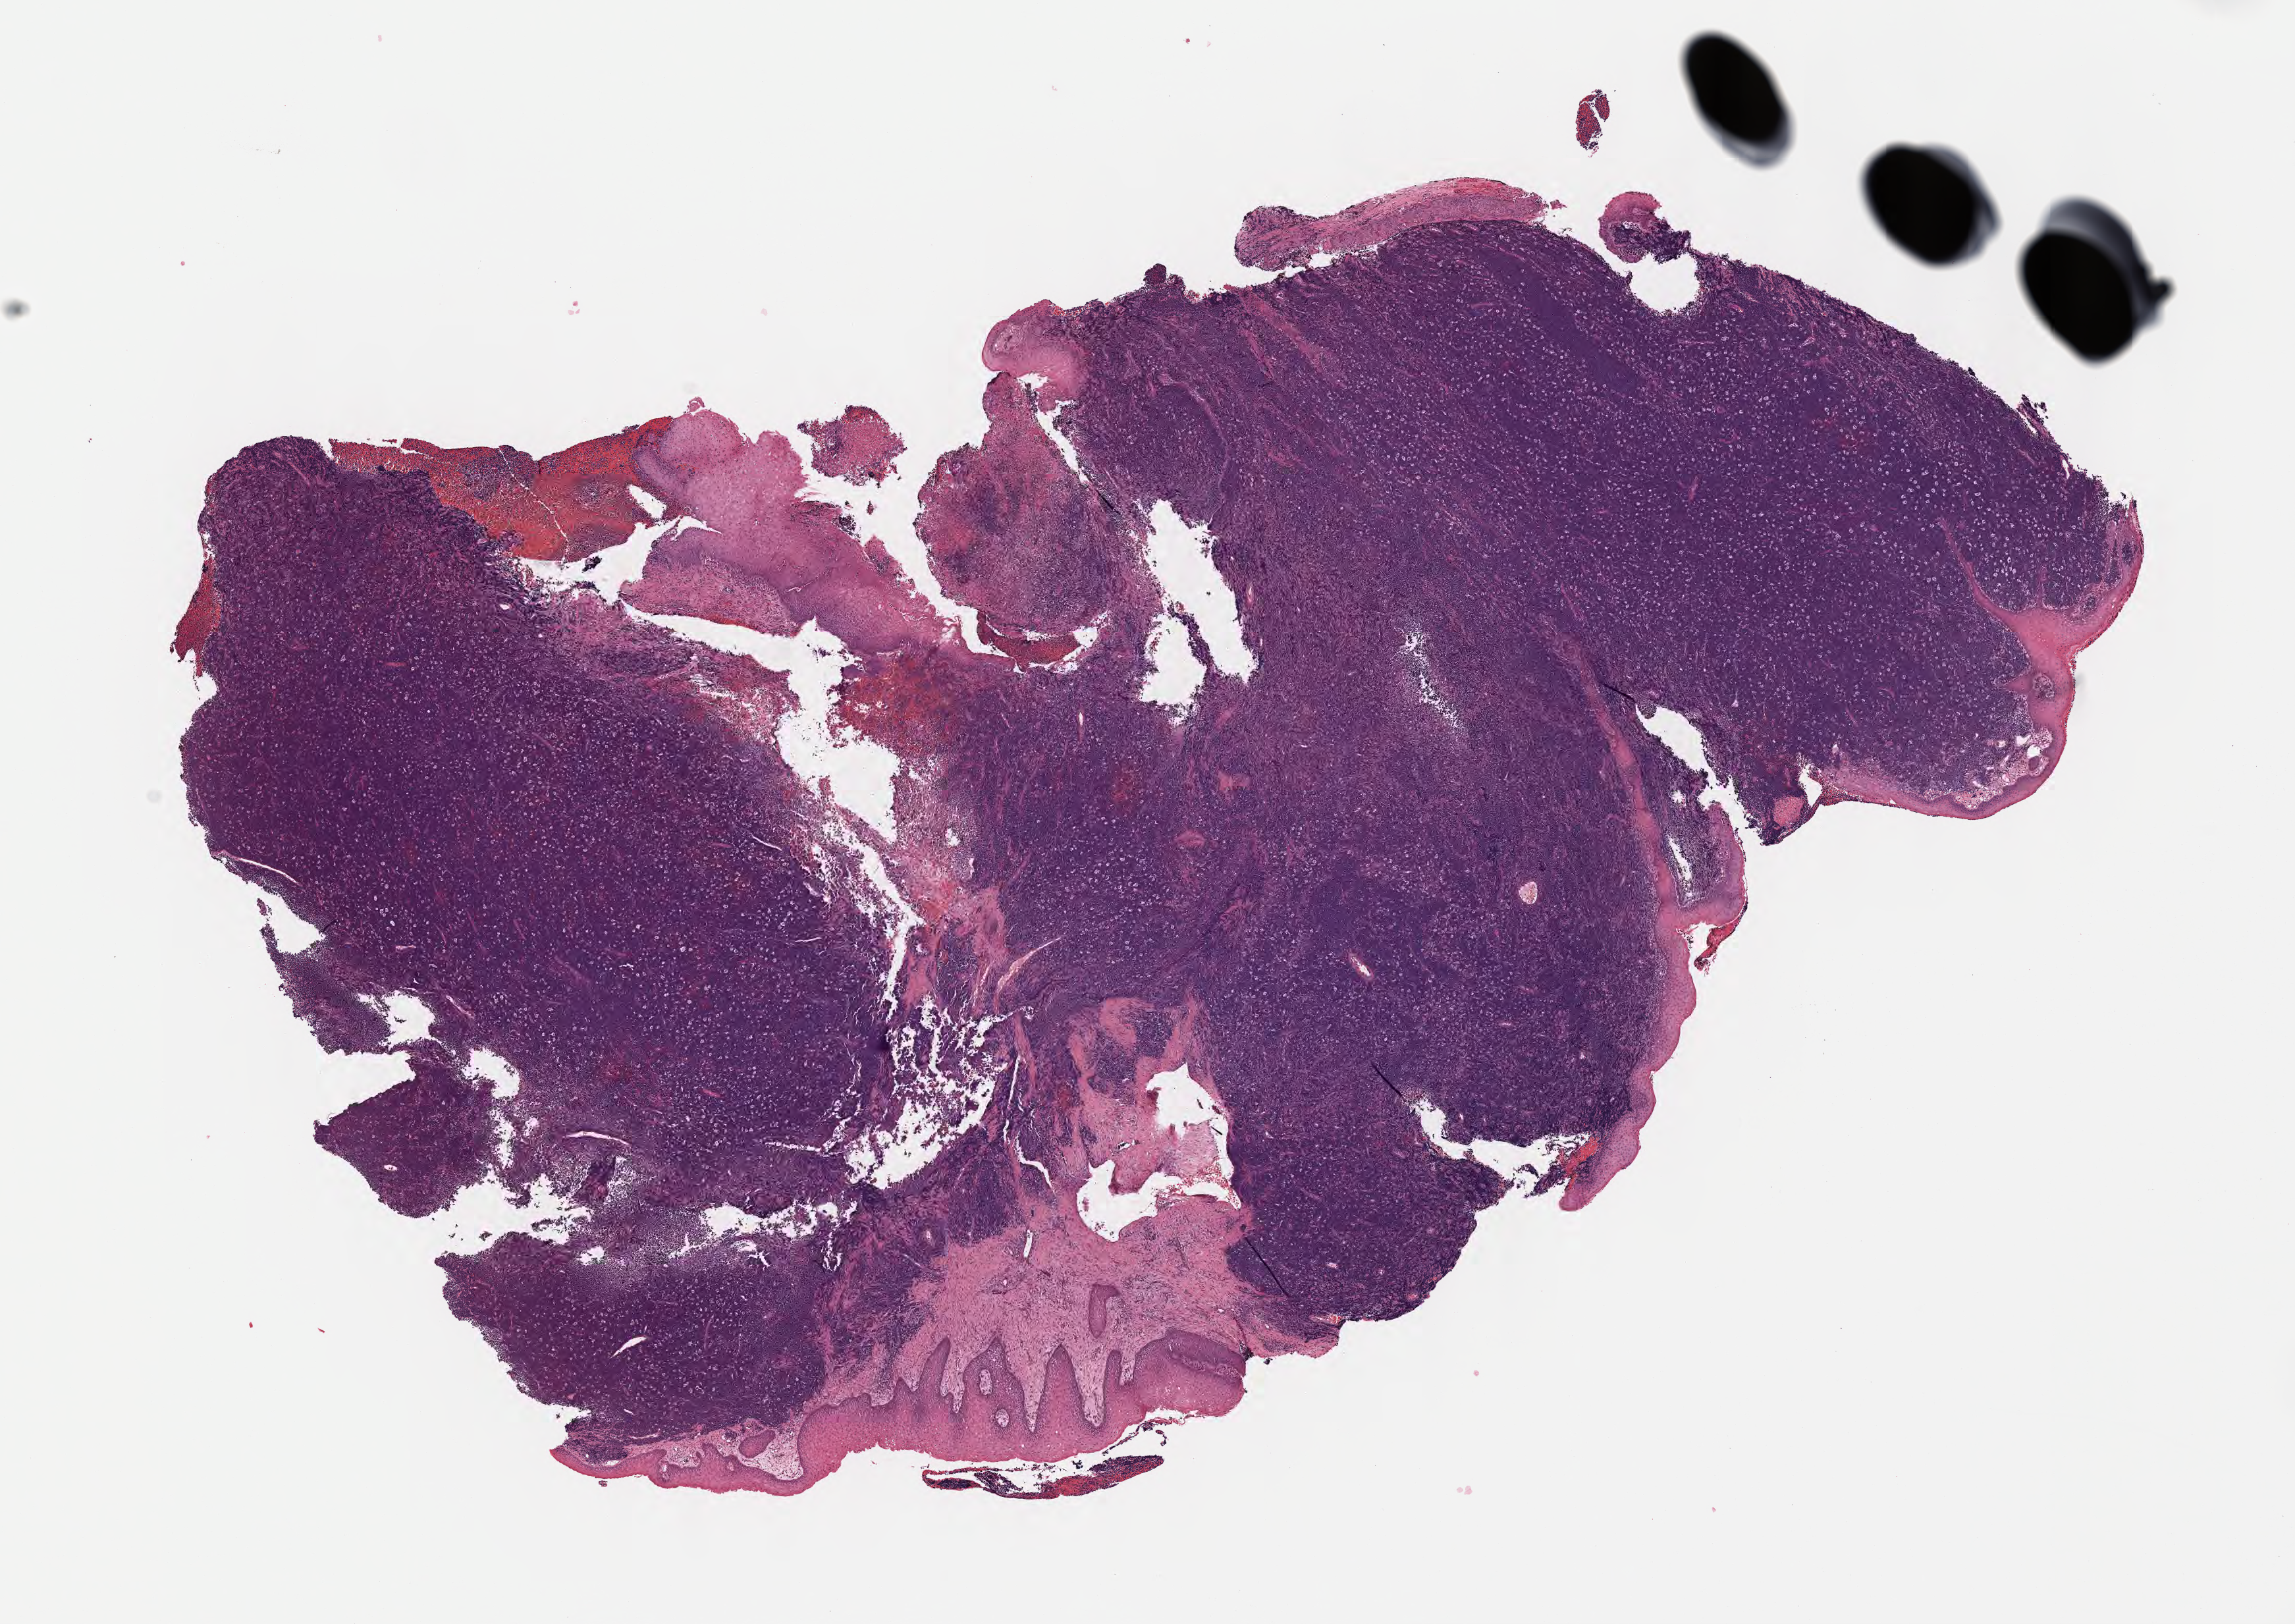
H&E whole-slide image — a low-resolution overview of the entire scanned area, about 14.1 x 10.0 mm, specimen: tumor tissue, site: cranium. Patient: male, age at initial diagnosis 4 years.
Diagnosis: Burkitt lymphoma, NOS.